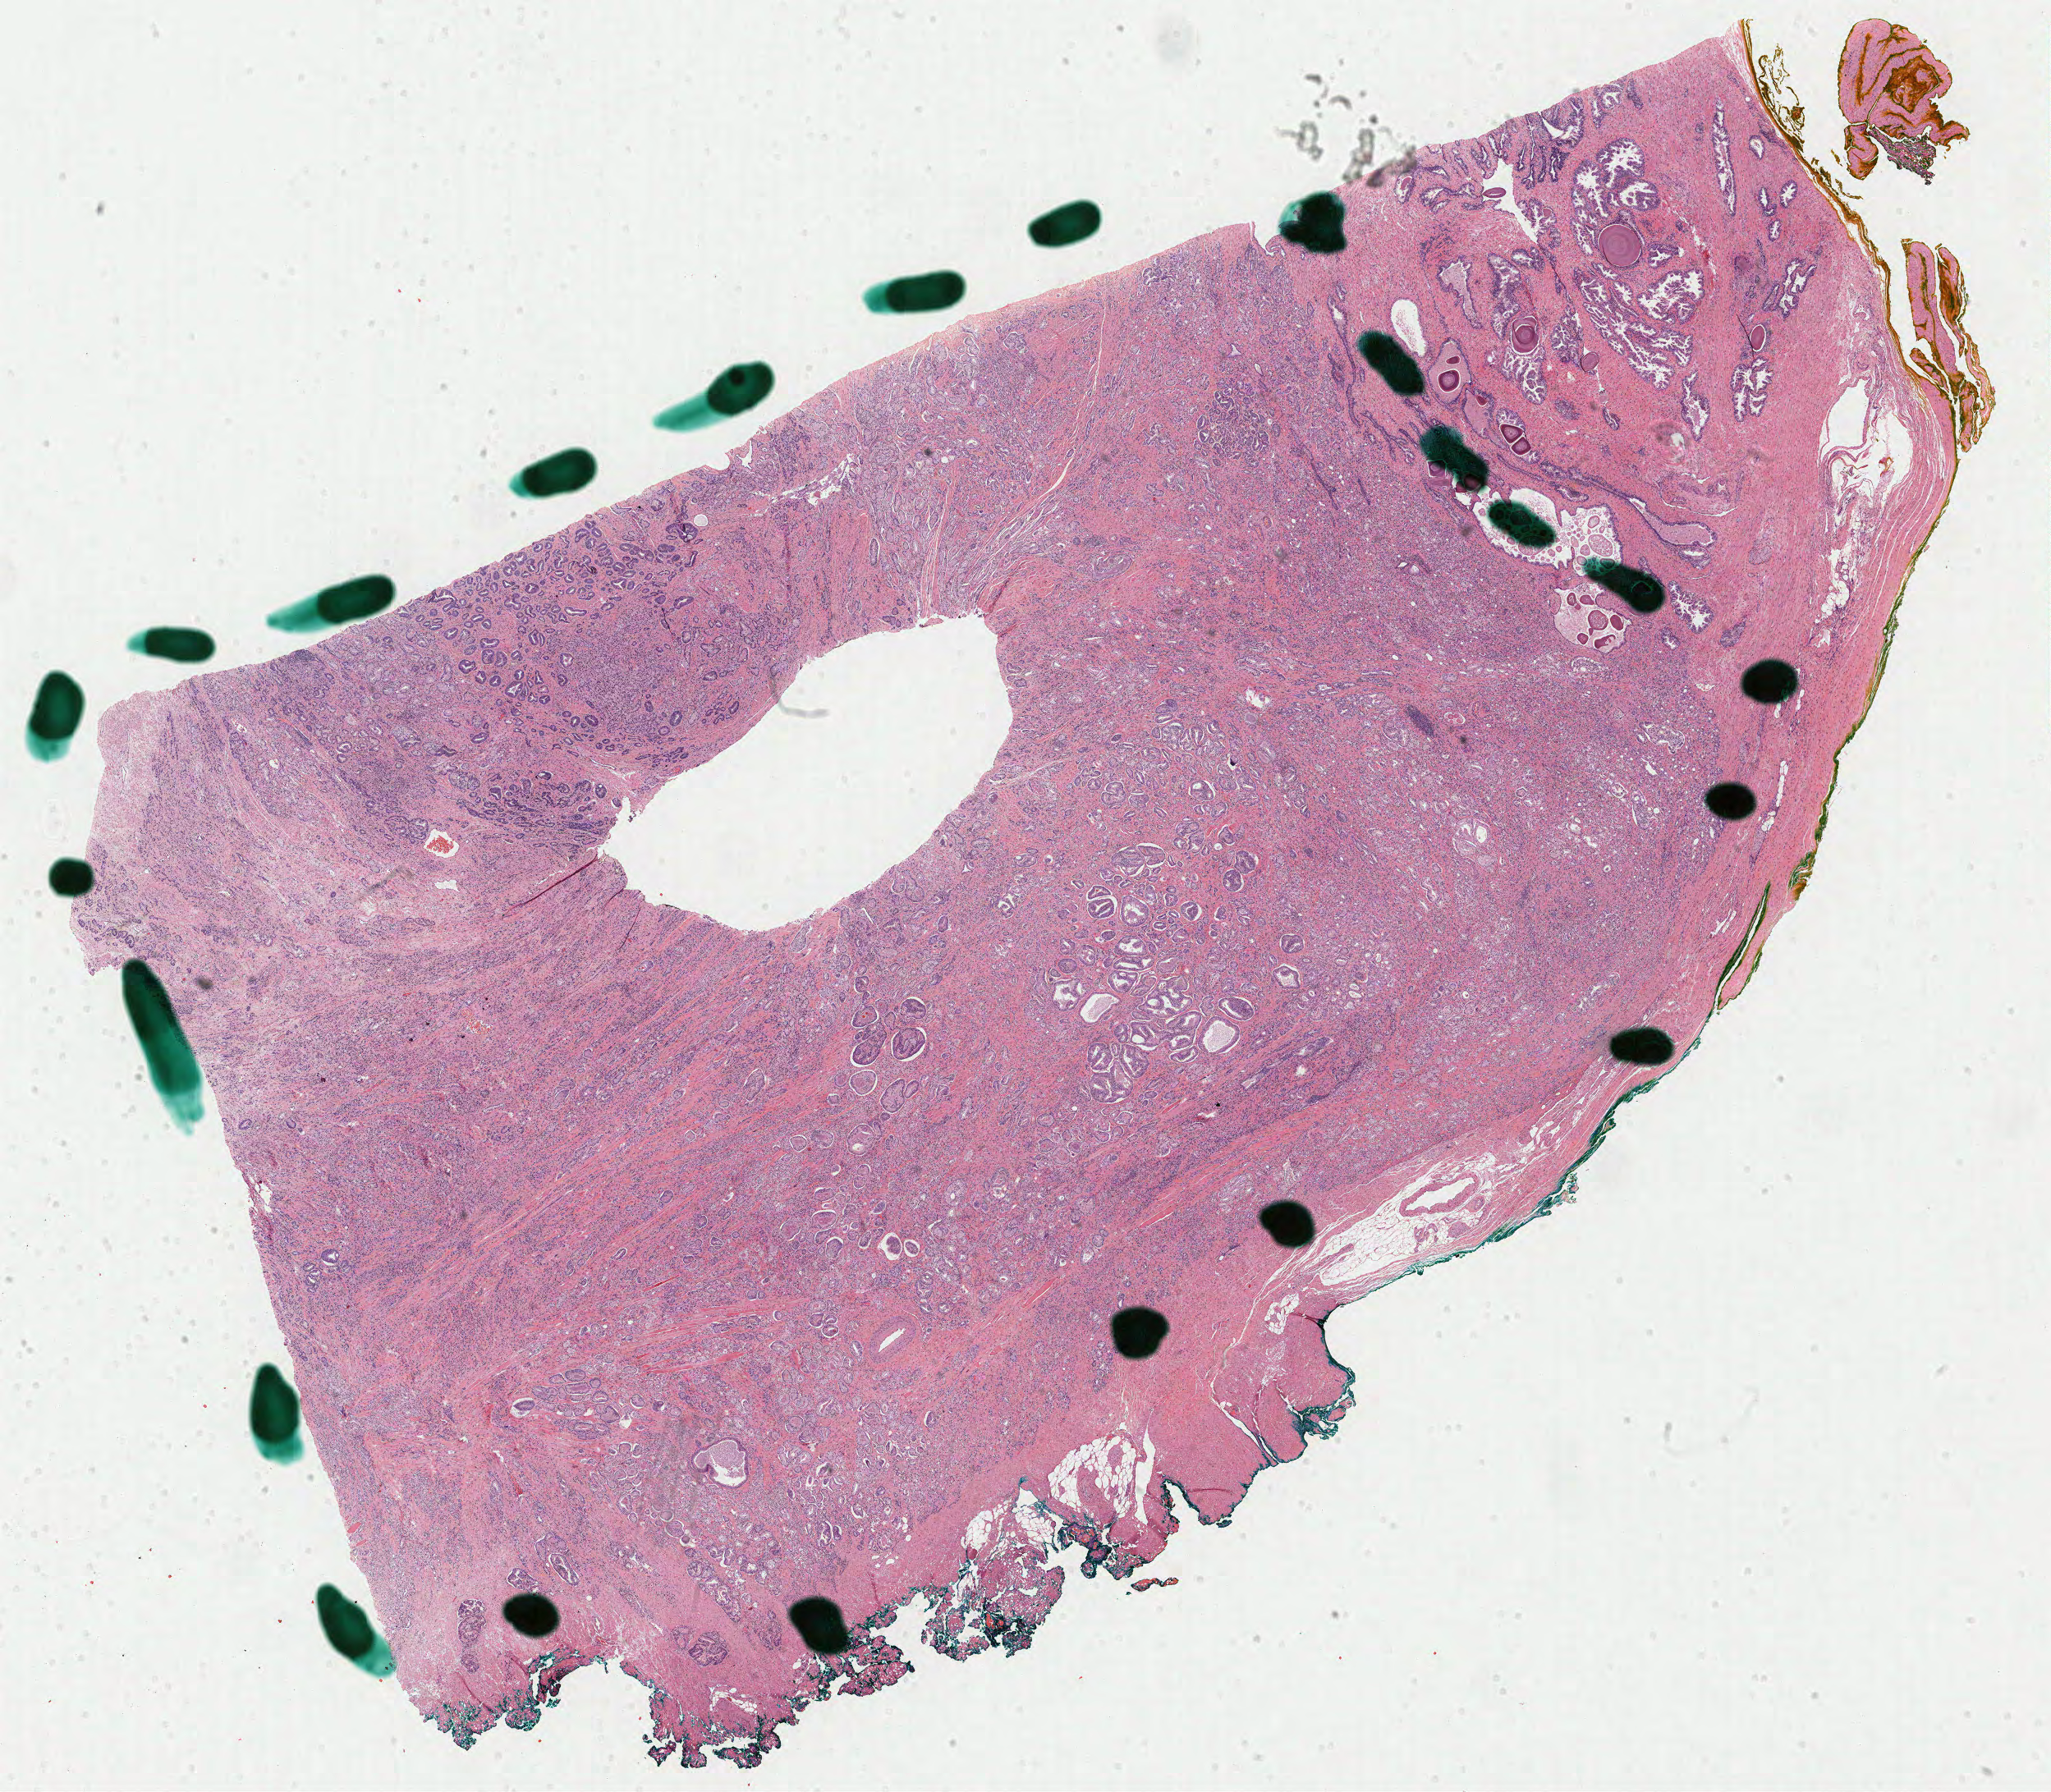
H&E-stained whole-slide image, low-resolution overview of the scanned area, about 19.8 x 17.3 mm (acquisition: 40x scan). Formalin-fixed paraffin-embedded (FFPE) diagnostic section. Primary tumour sample from the prostate. Patient: male, age at initial diagnosis 55 years. Gleason score: 7 (4+3).
- pathologic diagnosis: Adenocarcinoma, NOS